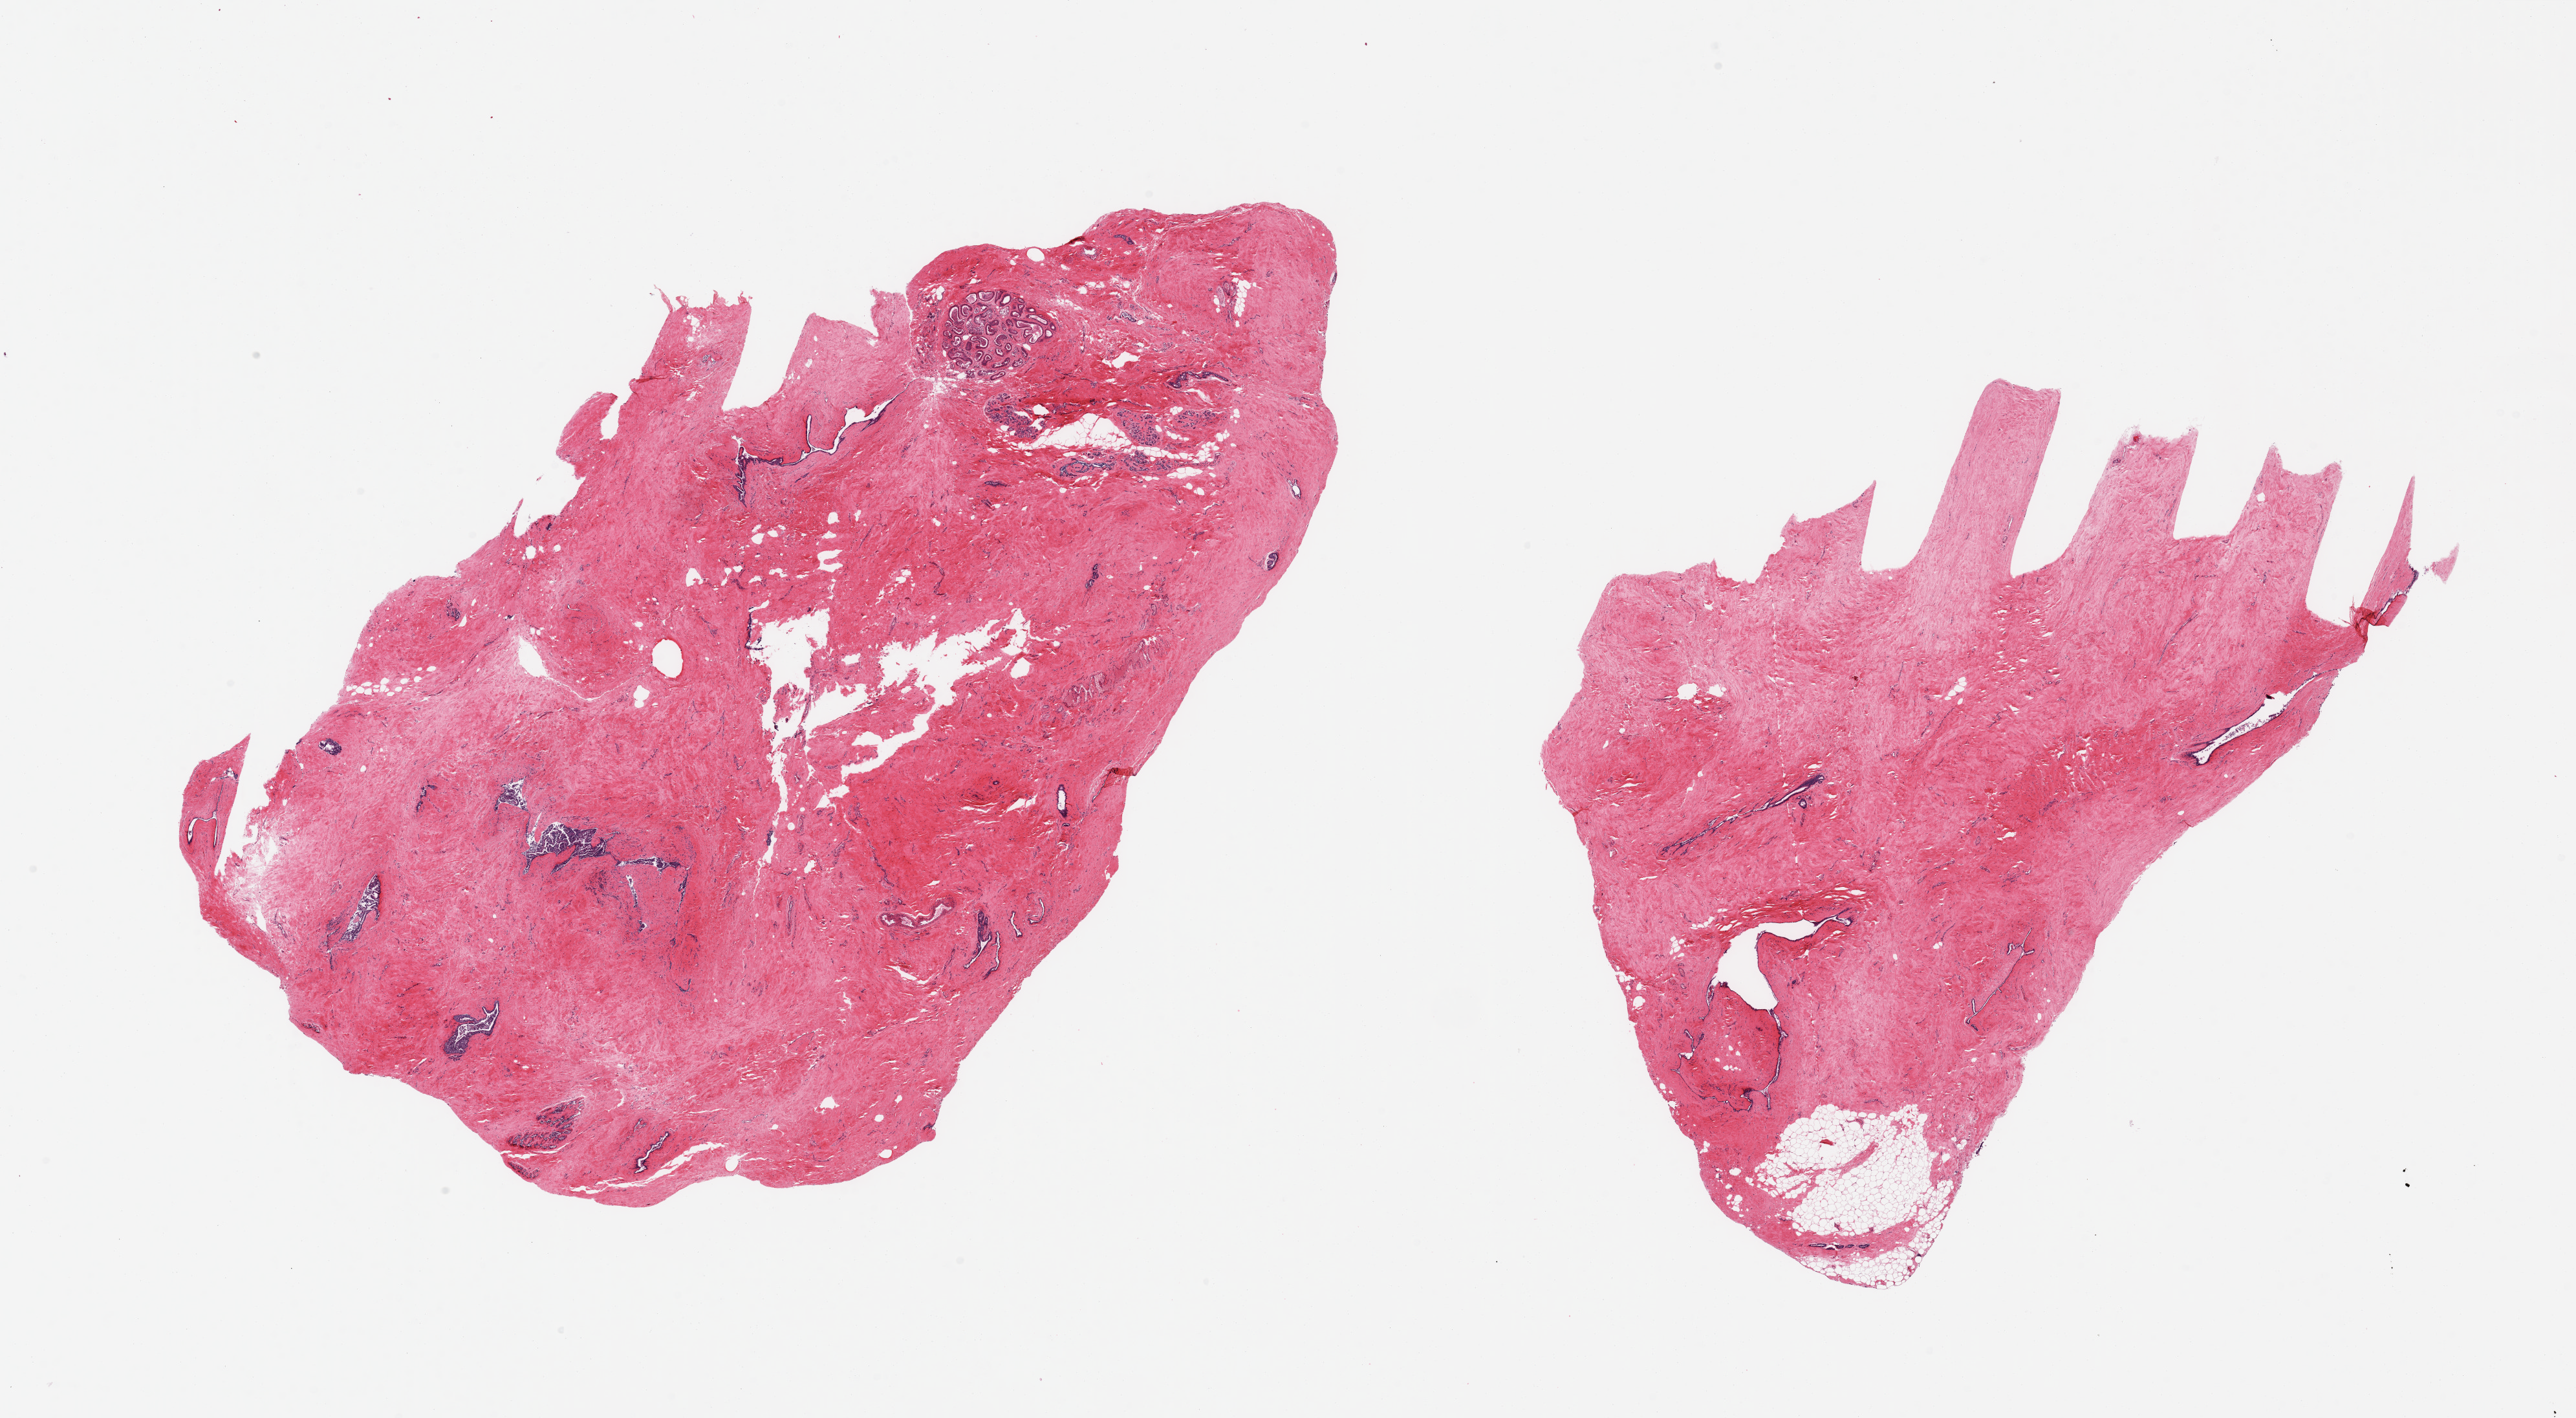
Digitized haematoxylin and eosin-stained section, brightfield — whole scanned area (about 31.5 x 17.3 mm, acquisition: 20x scan) shown as a low-resolution overview, PAXgene-fixed, paraffin-embedded tissue, sampled site (target tissue): breast, tissue donor sample. Male donor.
* pathologist's review note for this sample: 2 pieces gynecomastoid stromal and ductal ( rep) hyperplasia; unusual lobular elements